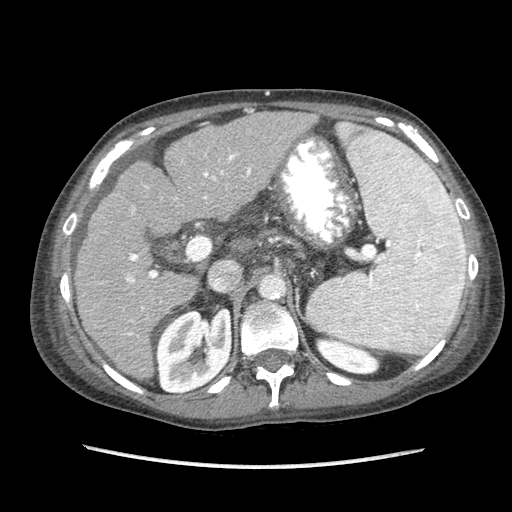
Contrast-enhanced abdominal CT (liver protocol), one axial slice; position 49 of 87 along the scan axis; 120 kVp; soft-tissue window (W 400 / L 40 HU); 2.5 mm slice thickness; 512 × 512 image matrix, field of view 340 × 340 mm. From the clinical record (not read from this slice): diagnosis: hepatocellular carcinoma (patient treated with transarterial chemoembolisation; whether this scan precedes or follows treatment is not stated here); TNM stage (as recorded): Stage-IIIB; Child-Pugh class: A; tumour differentiation: no biopsy; tumour nodularity: uninodular.
Annotated regions visible in this slice (semi-automatic segmentation, software-assisted and operator-edited):
- liver parenchyma outside the tumour (the mass and vessels are separate outlines, so this box may not span the whole liver): bounding box (x1, y1, x2, y2) in pixels: (74, 112, 316, 380)
- liver vessels: (126, 153, 251, 336)